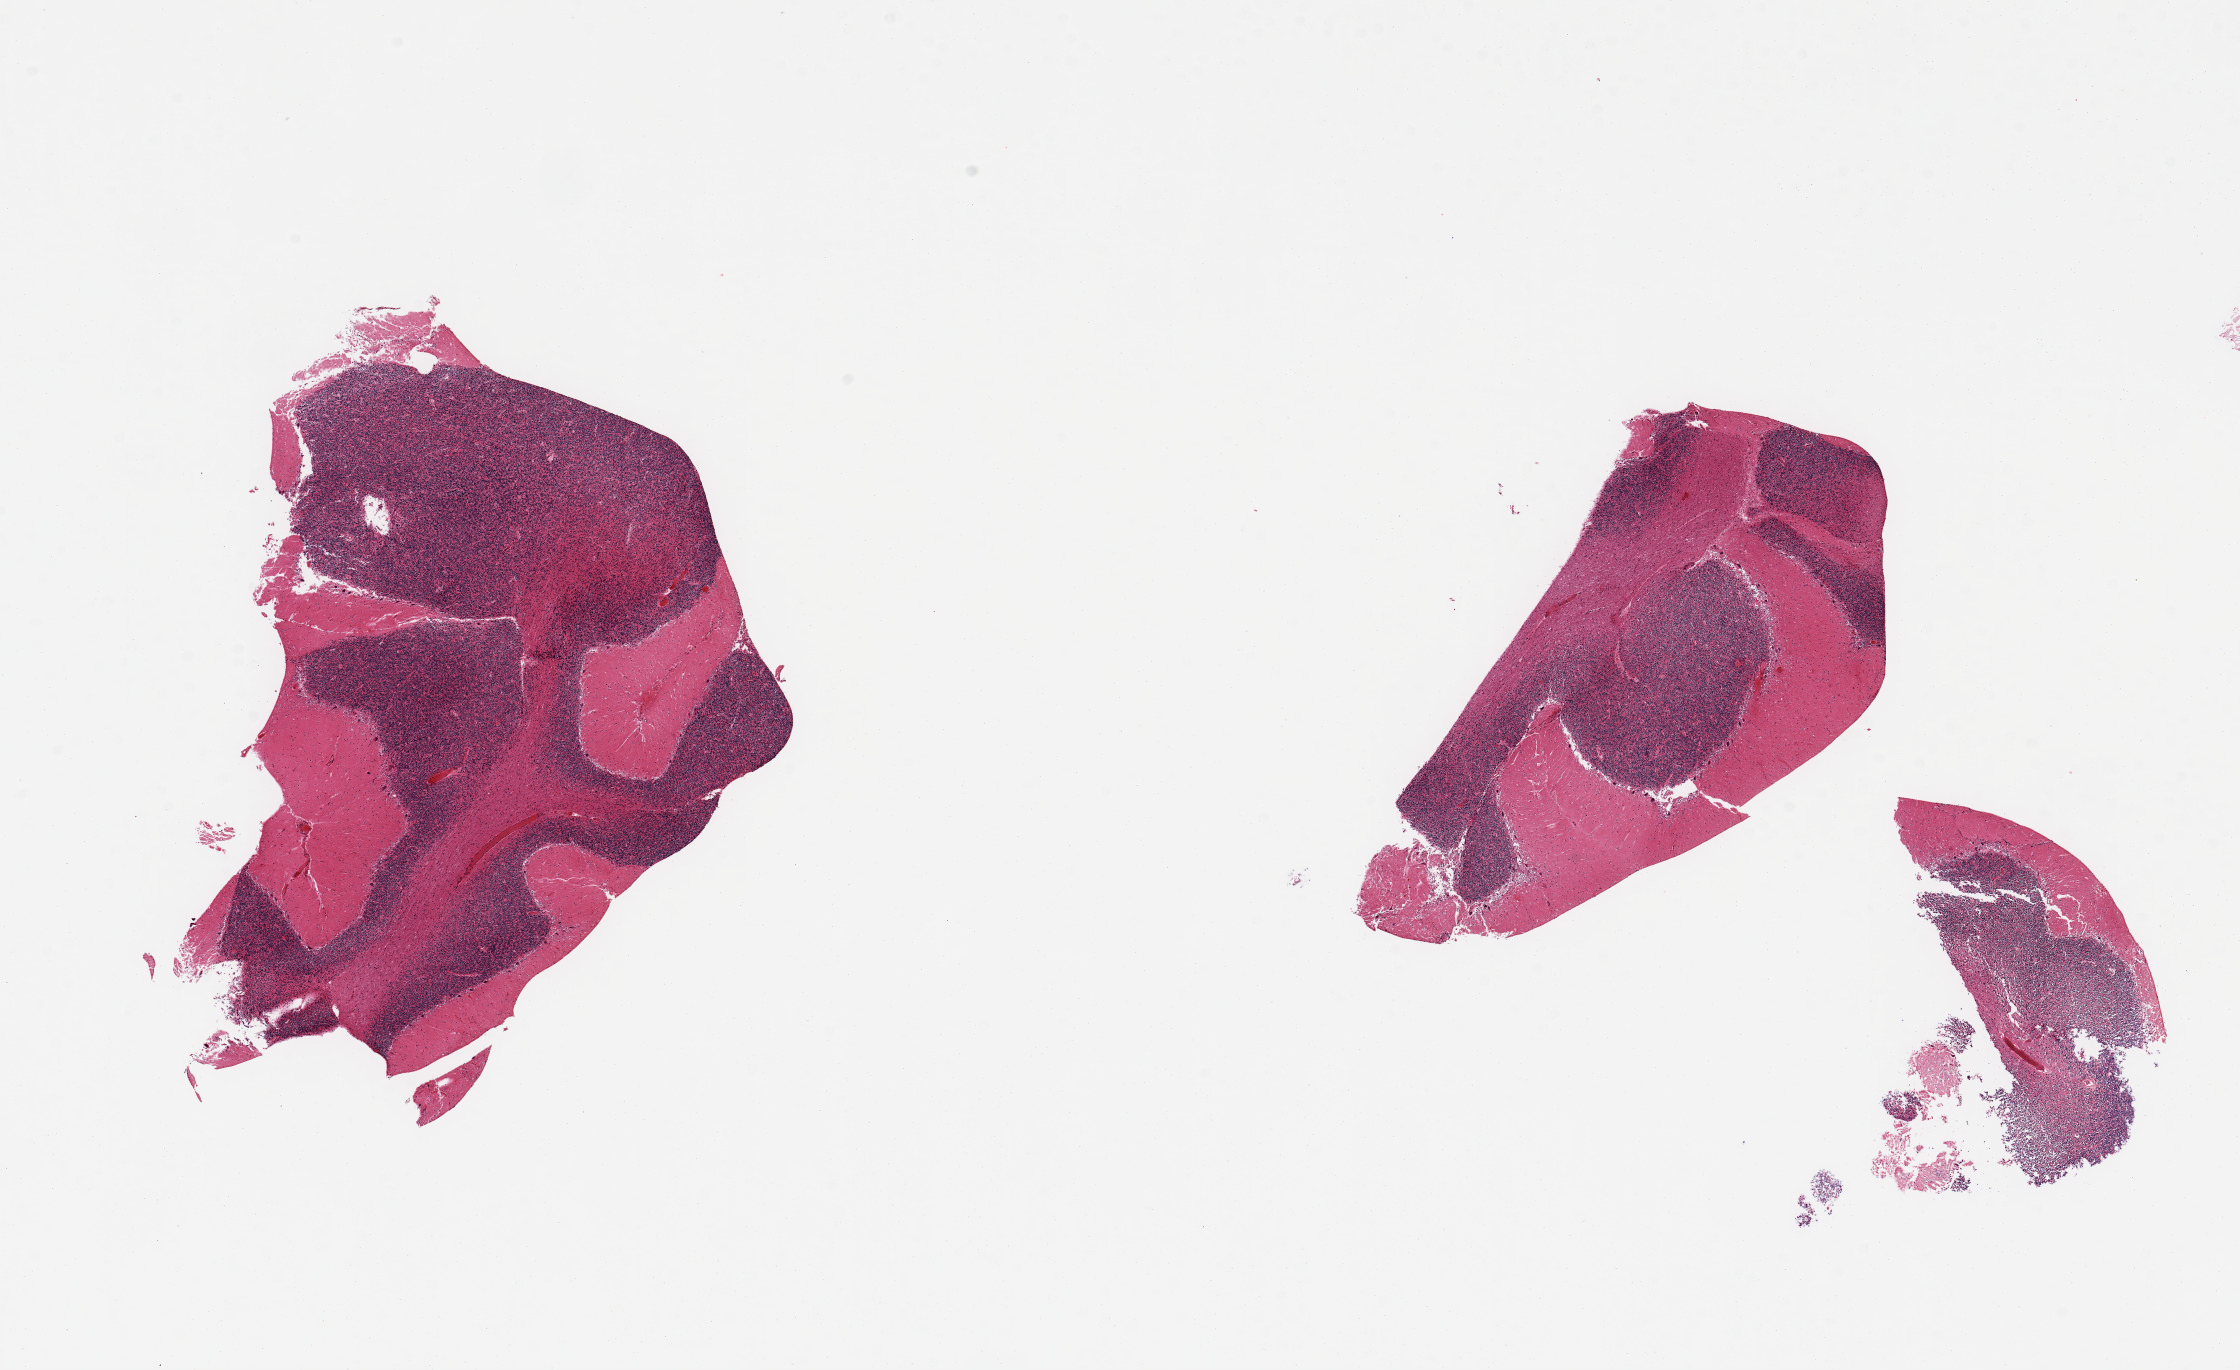
Hematoxylin and eosin (H&E) whole-slide image — shown as a low-resolution overview of the whole scanned area (about 17.7 x 10.8 mm, acquisition: 20x scan), PAXgene-fixed, paraffin-embedded tissue, section of cerebellum (target tissue), donor tissue sample.
Review note (as recorded): 2 pieces; some fragmentation.